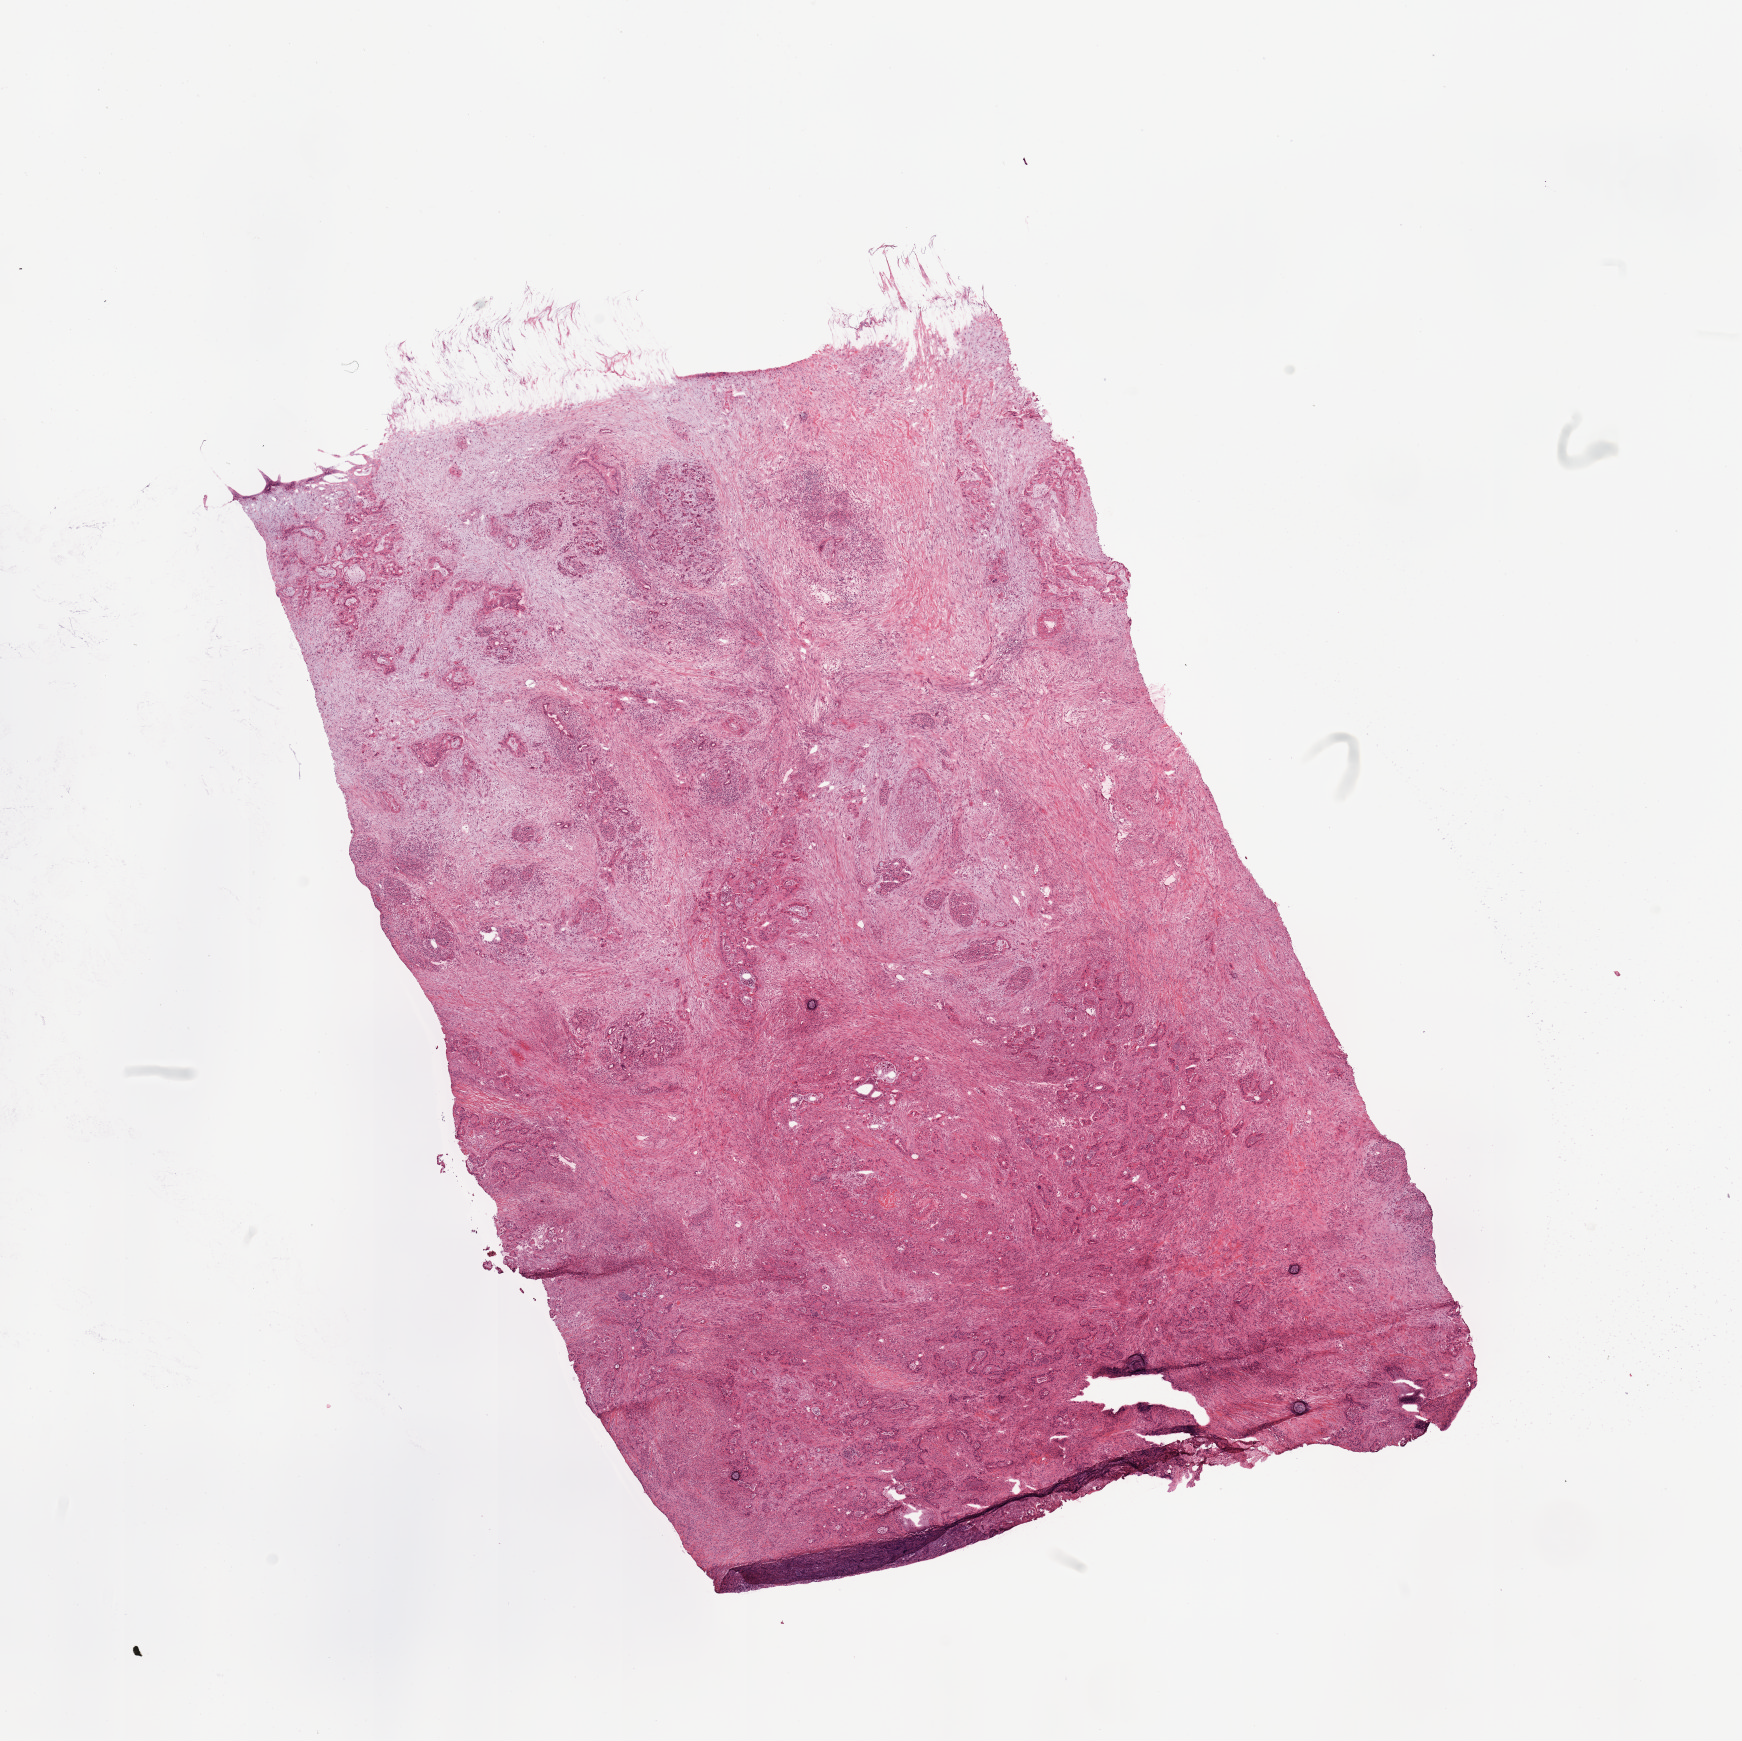
Digitized Hematoxylin and eosin (H&E) stained tissue section (whole slide) — a low-resolution overview of the entire scanned area, about 13.8 x 13.8 mm. Tumour tissue sample, sampled site: pancreas. Patient: female, age 62 years. Histologic grade: G2 (moderately differentiated). Pathologist review of this section (percent, as recorded): tumour nuclei 40%, necrosis 0%.
AJCC pathologic stage: IIB. Primary tumour site (as recorded): body. Histologic diagnosis: Infiltrating duct carcinoma, NOS.